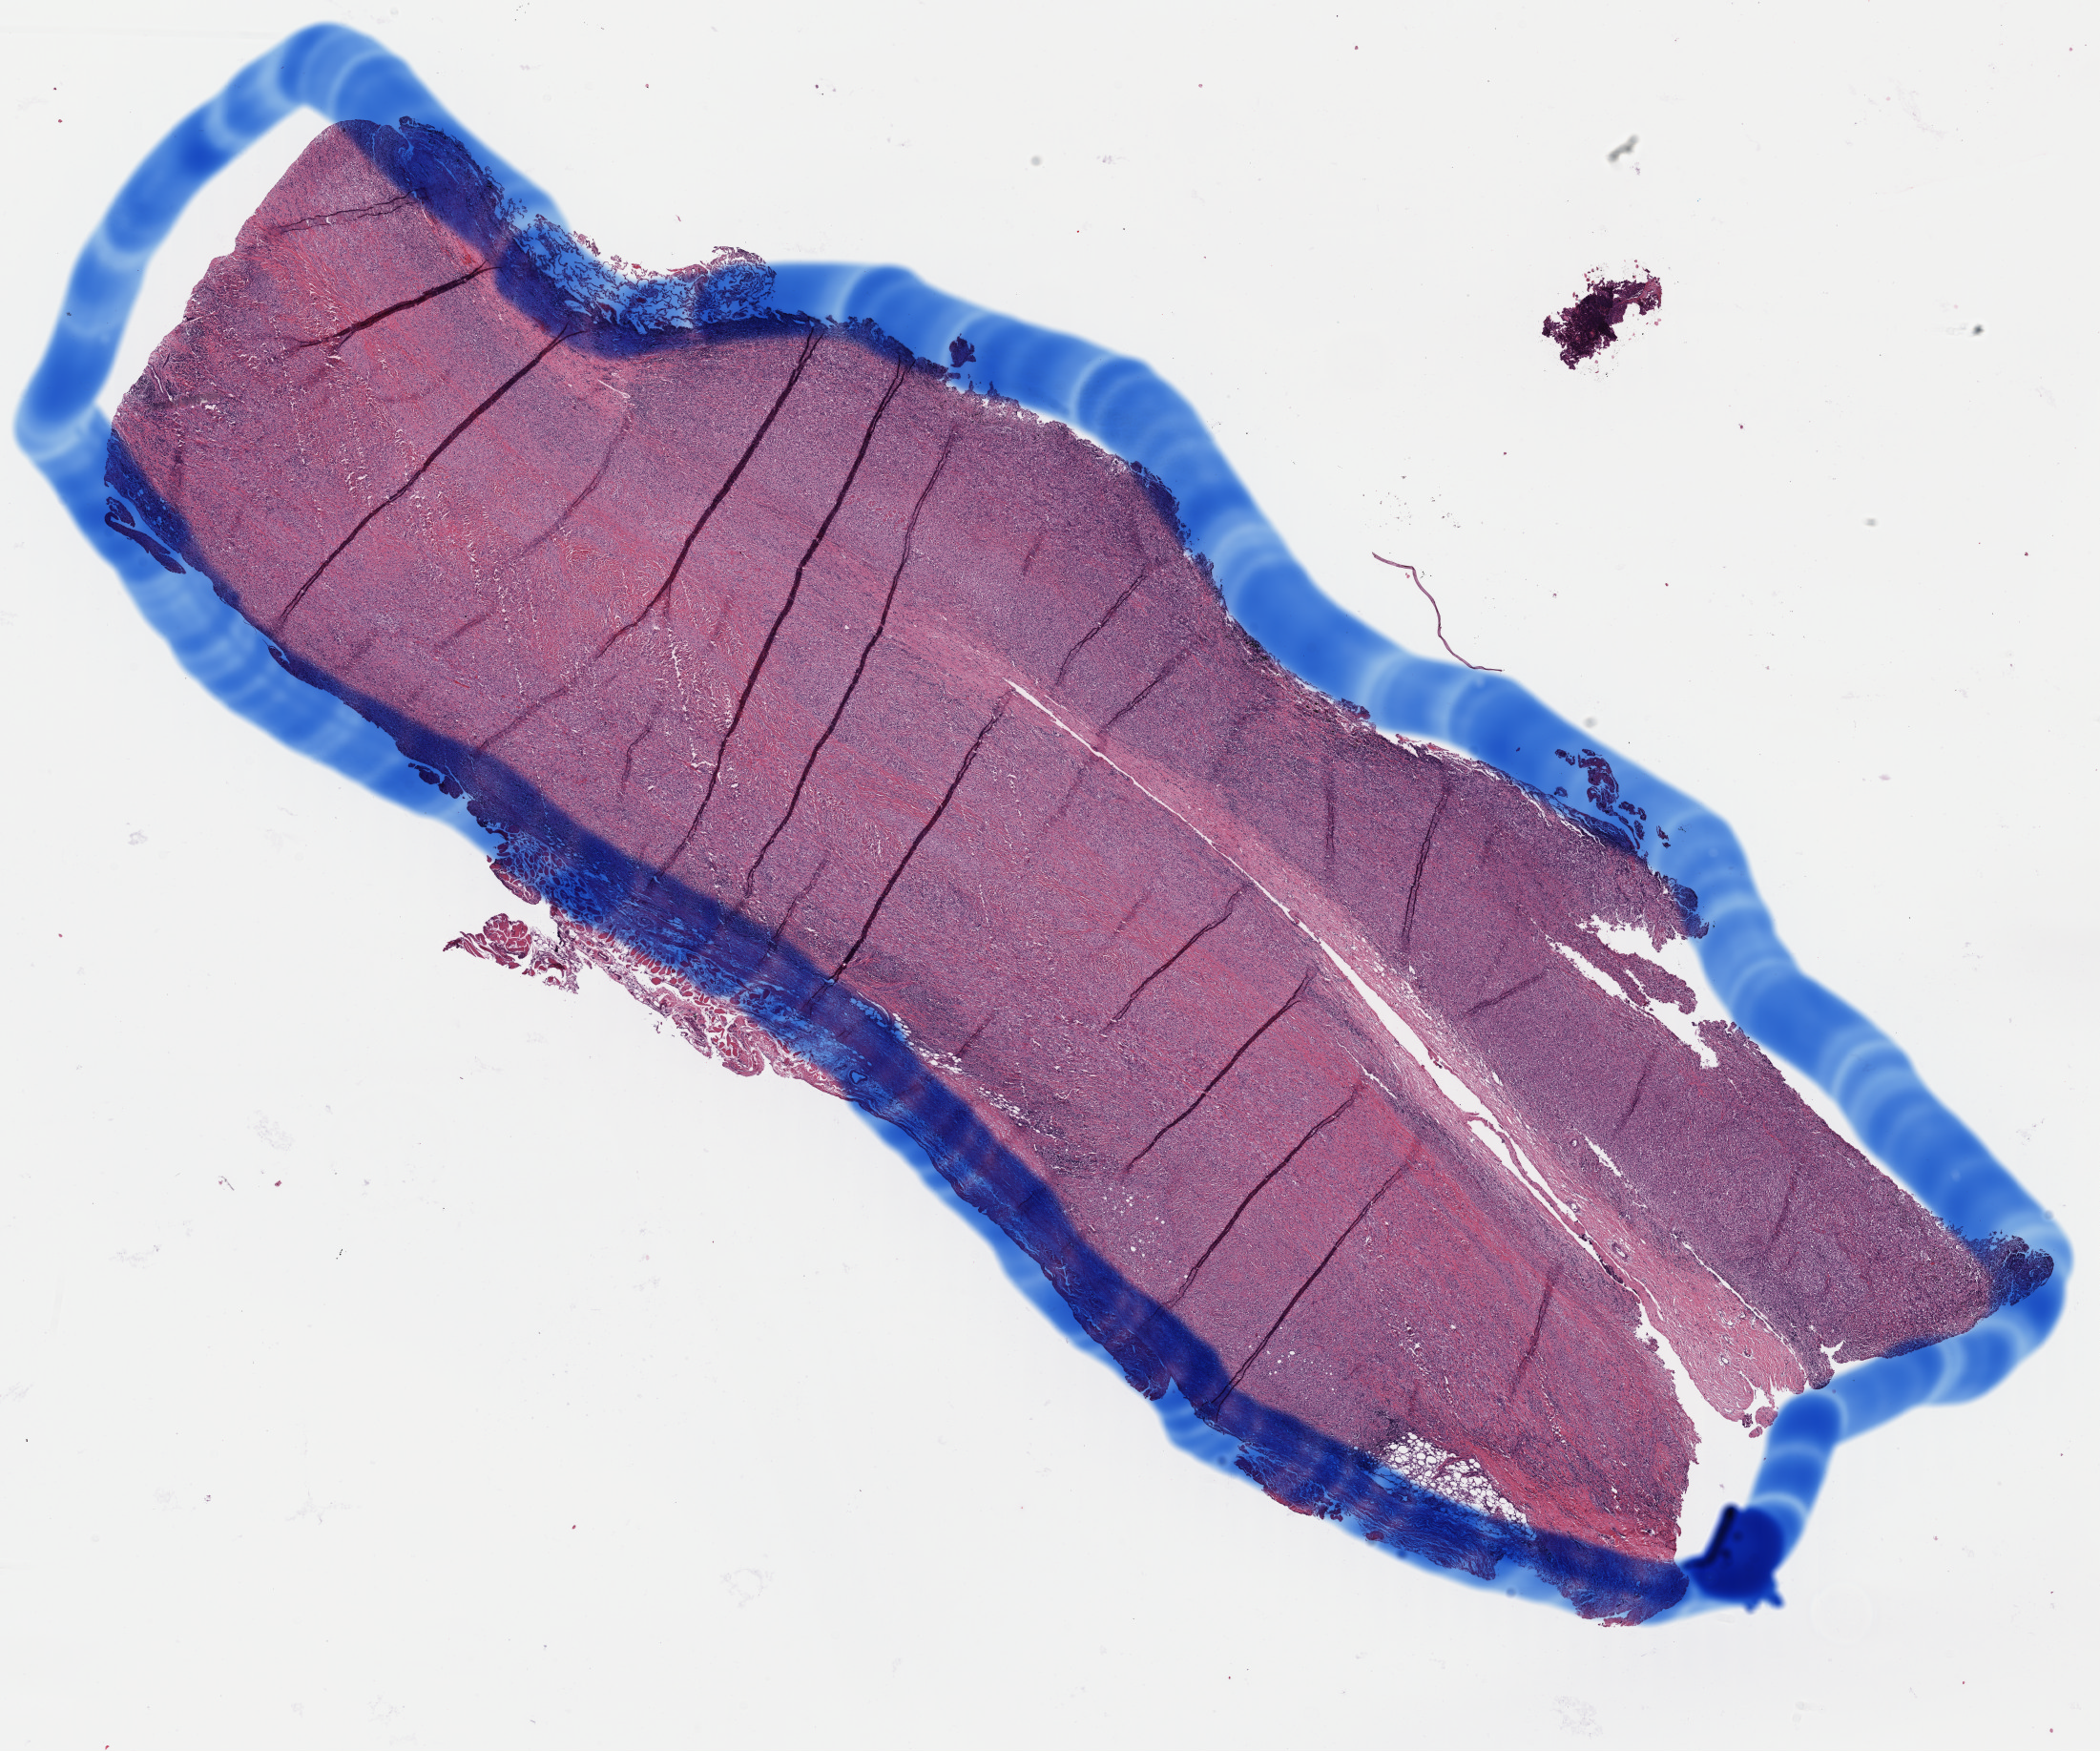
Digitized Hematoxylin and eosin (H&E) stained tissue section (whole slide), shown as a low-resolution overview of the whole scanned area (about 17.4 x 14.5 mm), formalin-fixed paraffin-embedded (FFPE) diagnostic section, sample: primary tumour, mesothelium. Male patient; age at initial diagnosis 78 years.
* pathologic diagnosis: Mesothelioma, biphasic, malignant (pleura, NOS)
* laterality: right
* AJCC pathologic stage: II (6th edition)